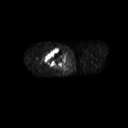
FDG PET of an extremity soft-tissue mass (from a PET/CT study), one axial slice. Position 251 of 311 along the scan axis. 3.27 mm slice thickness. 128 × 128 image matrix. Male patient, age 50 years. Case-level facts recorded for this patient, not image findings: histological type: undifferentiated - pleiomorphic; grade: high; site of the primary tumour: right thigh.
Annotated regions visible in this slice (expert contour drawn on MRI and transferred to this co-registered scan by the dataset authors):
- gross tumour volume including surrounding oedema: bounding box <42,49,64,66> (left, top, right, bottom; pixels)
- gross tumour volume (mass): <45,49,64,66>